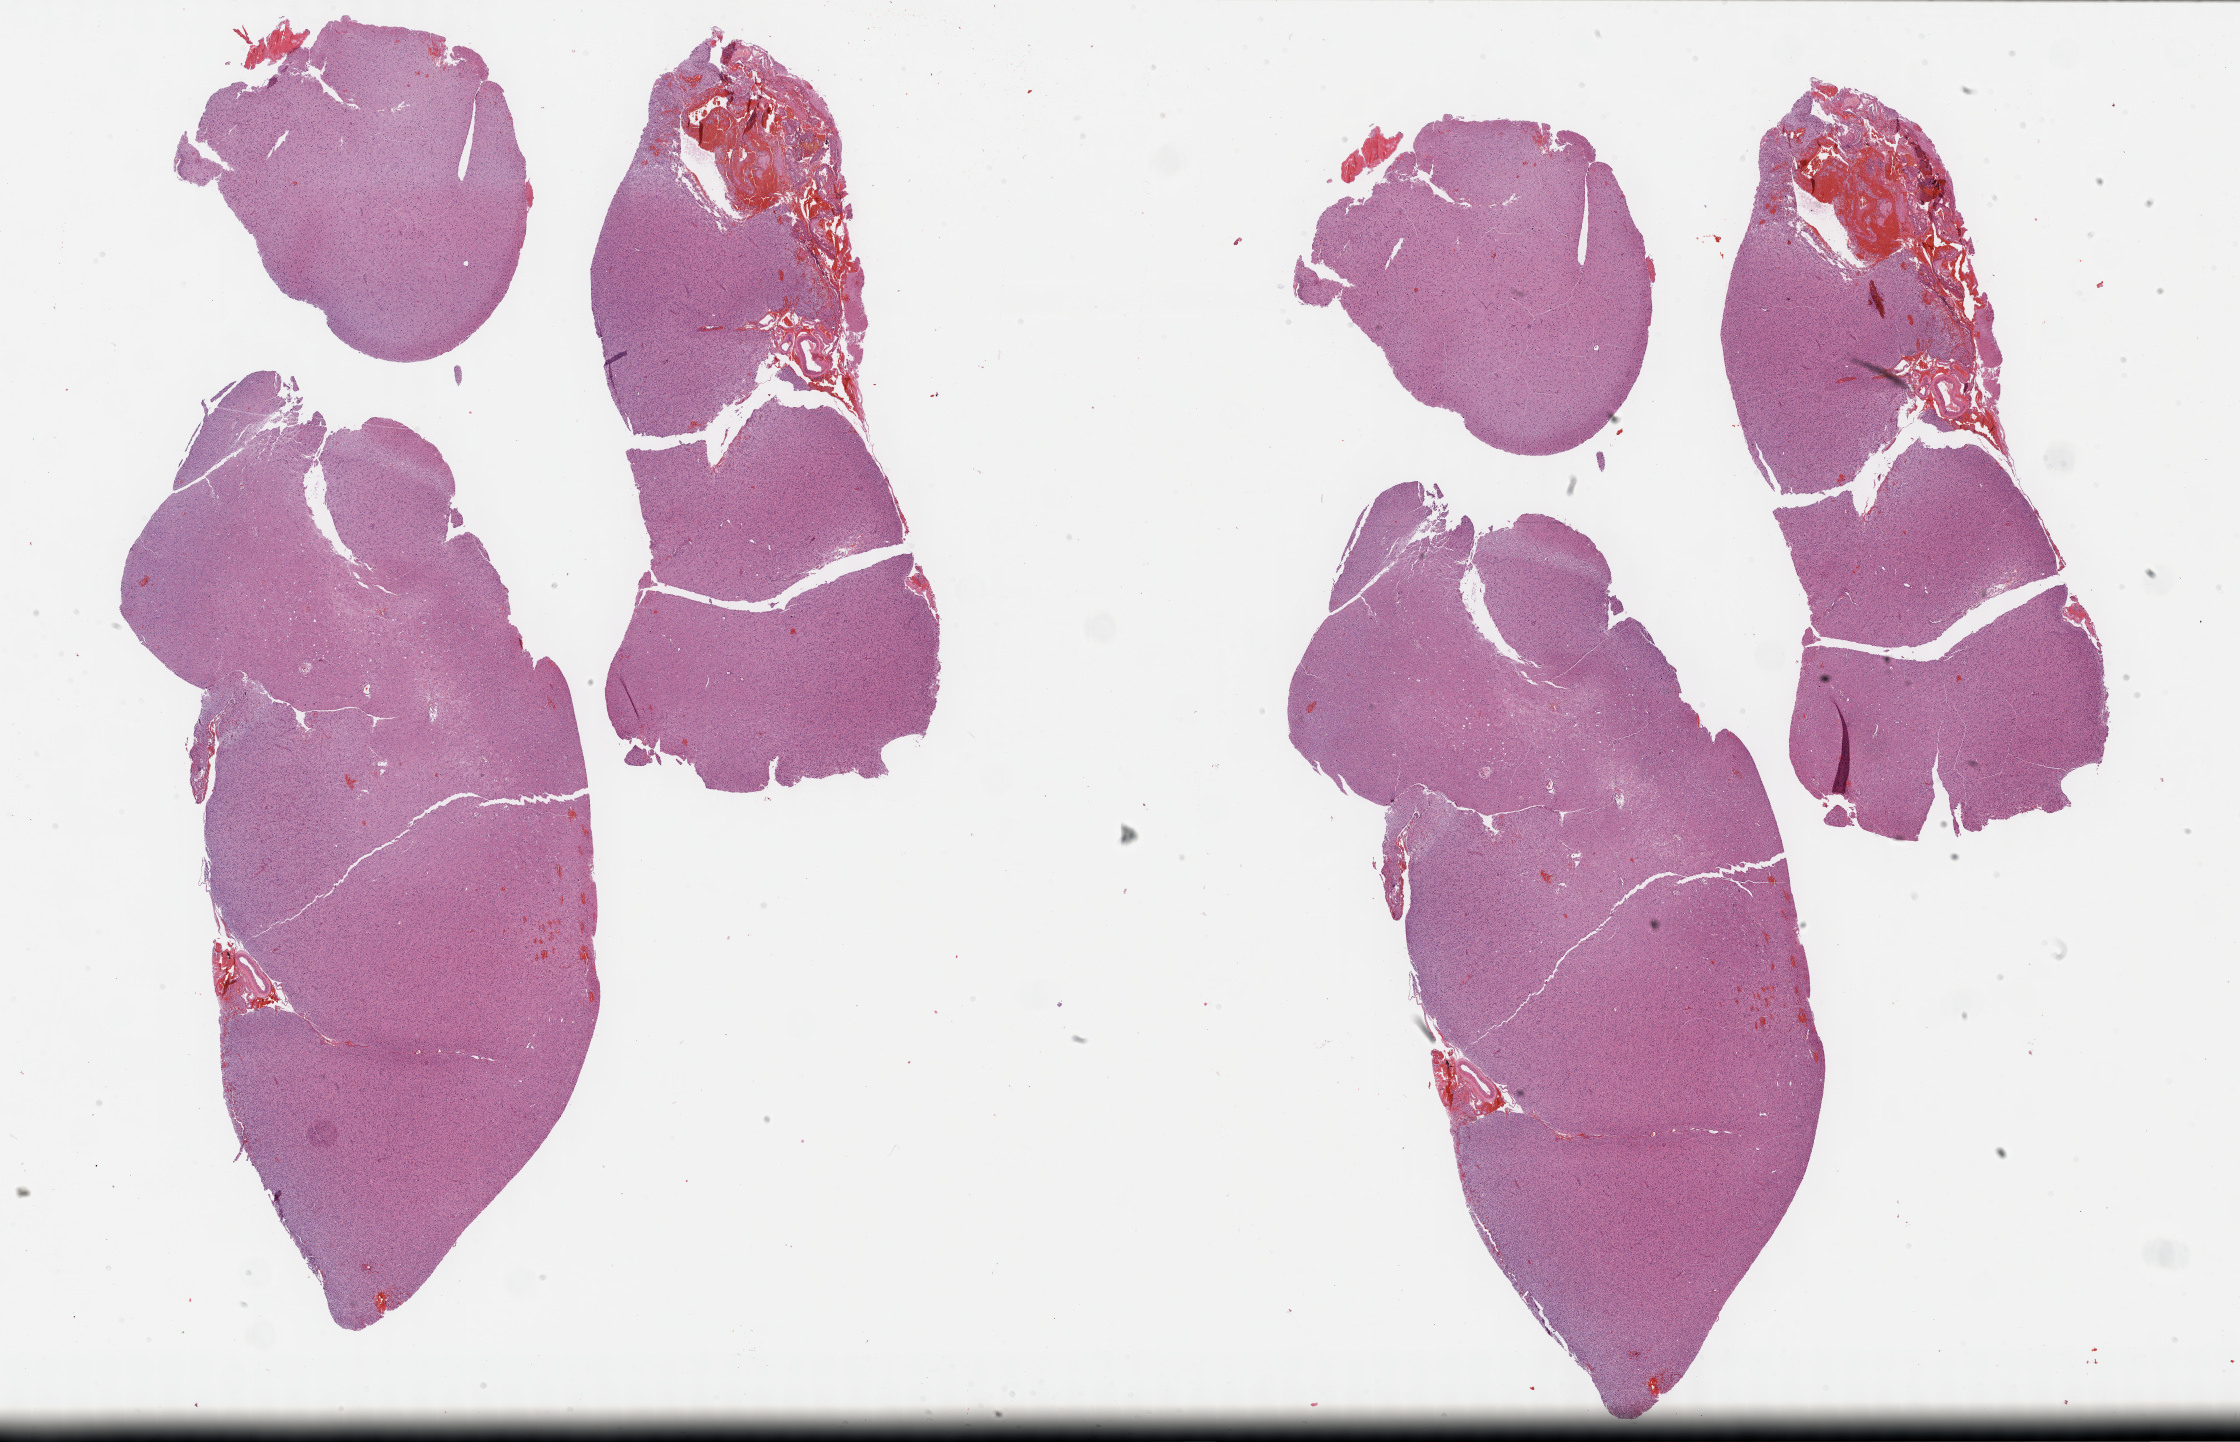
Digitized H&E tissue section (whole slide), a low-resolution overview of the entire scanned area, about 36.2 x 23.3 mm, formalin-fixed paraffin-embedded (FFPE) diagnostic section, sample: primary tumour, brain. Female, age 61 years at initial diagnosis. Histologic grade: G3 (poorly differentiated).
* laterality: right
* diagnosis: Astrocytoma, anaplastic (cerebrum)